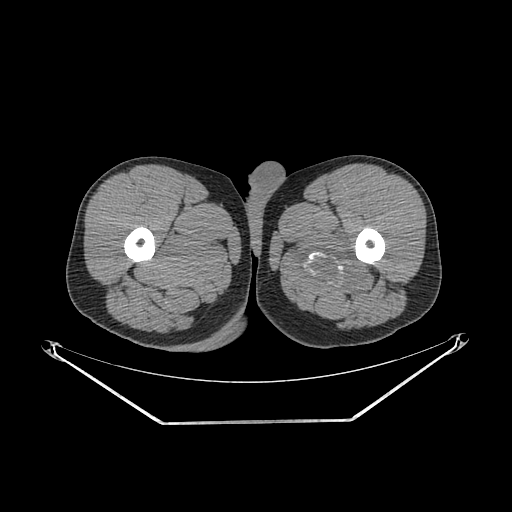
CT of an extremity soft-tissue mass (from a PET/CT study), one axial slice. Slice 253 of 267 in the series (ordered by position). Reconstruction kernel SOFT. 140 kVp. Soft-tissue window (W 400 / L 40 HU). 3.75 mm slice thickness. 512 × 512 image matrix, field of view 500 × 500 mm. Male patient. Case-level facts recorded for this patient, not image findings: histological type: extraskeletal osteosarcoma; grade: high; site of the primary tumour: left adductur.
Outlined on this slice (expert contour drawn on MRI and transferred to this co-registered scan by the dataset authors):
- gross tumour volume (mass): box from (x=288, y=222) to (x=378, y=298) px